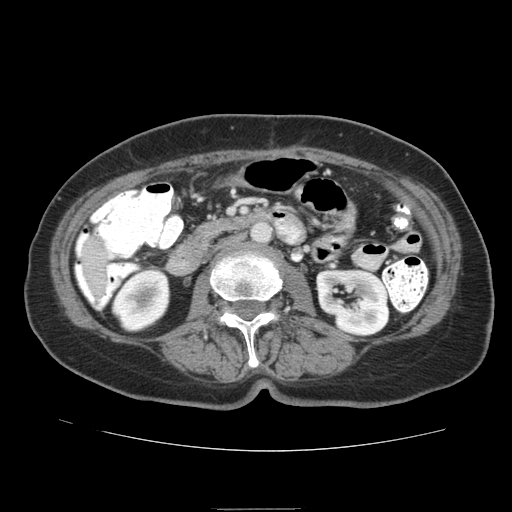
Contrast-enhanced abdominal CT (liver protocol), one axial slice; position 21 of 95 along the scan axis; 140 kVp; soft-tissue window (W 400 / L 40 HU); 2.5 mm slice thickness; 512 × 512 image matrix, field of view 360 × 360 mm. From the clinical record (not read from this slice): diagnosis: hepatocellular carcinoma (patient treated with transarterial chemoembolisation; whether this scan precedes or follows treatment is not stated here); TNM stage (as recorded): Stage-IVA; Child-Pugh class: B; tumour differentiation: moderately differentiated; tumour nodularity: uninodular.
Structures marked on this image (semi-automatically segmented with operator editing):
- liver parenchyma outside the tumour (the mass and vessels are separate outlines, so this box may not span the whole liver): bounding box (x1, y1, x2, y2) in pixels: (76, 234, 110, 280)
- liver vessels: (76, 234, 88, 256)